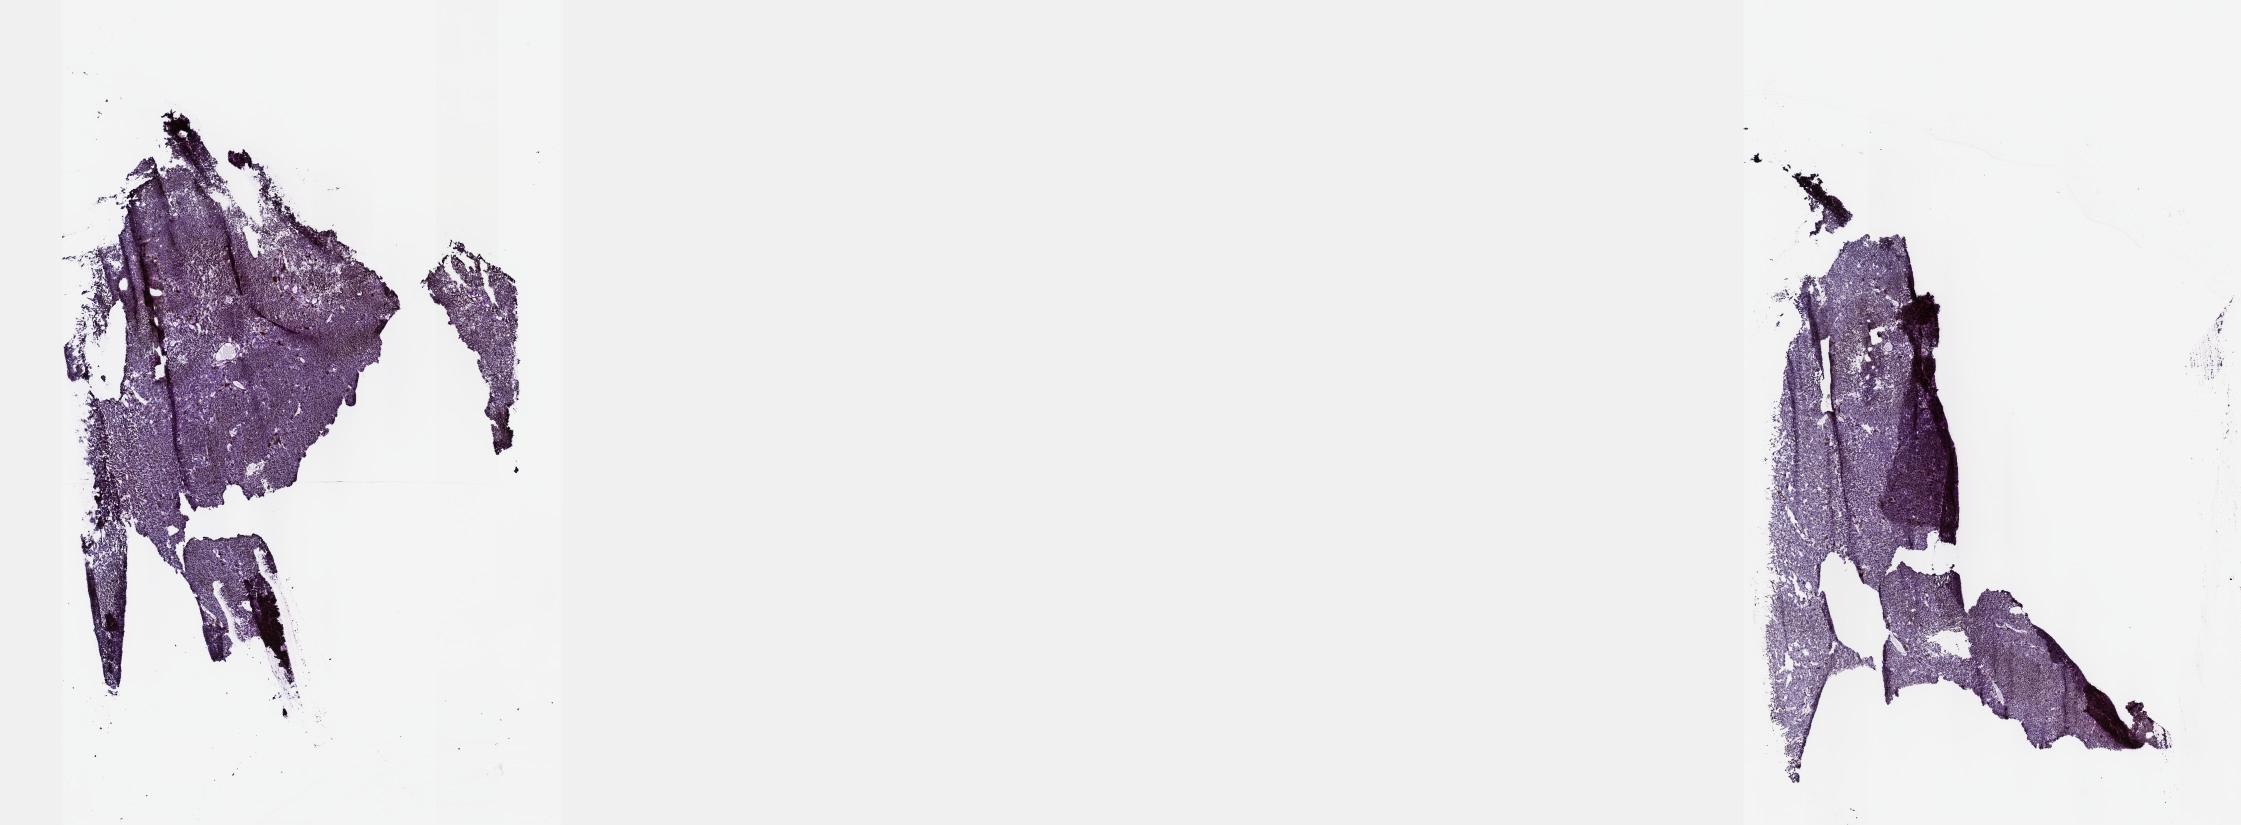
Whole-slide histology image, Hematoxylin and eosin (H&E) stained — whole scanned area (about 18.1 x 6.7 mm) shown as a low-resolution overview; frozen section from the top of the tissue portion; uvea, primary tumour sample. Male patient; age at initial diagnosis 64 years. Composition of this section per pathologist review: tumour cells 100%, tumour nuclei 80%, normal cells 0%, stromal cells 0%, necrosis 0%. Infiltration values recorded for this section: lymphocyte infiltration 1%, monocyte infiltration 0%, neutrophil infiltration 0%.
• histologic diagnosis: Mixed epithelioid and spindle cell melanoma (choroid)
• AJCC pathologic stage: IIIA (7th edition)